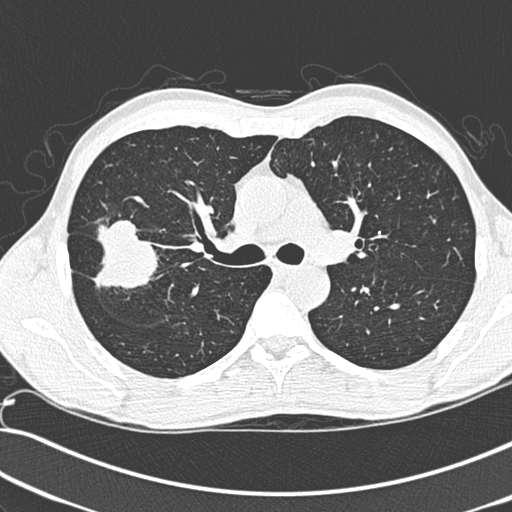
Low-dose screening chest CT, one axial slice. Position 193 of 281 along the scan axis. 120 kVp. Lung window (W 1500 / L -600 HU). 512 × 512 image matrix, field of view 341 × 341 mm.
Annotated regions visible in this slice (expert manual segmentation):
- lesion 1 (tumor, upper lobe of right lung): box from (x=92, y=219) to (x=158, y=295) px